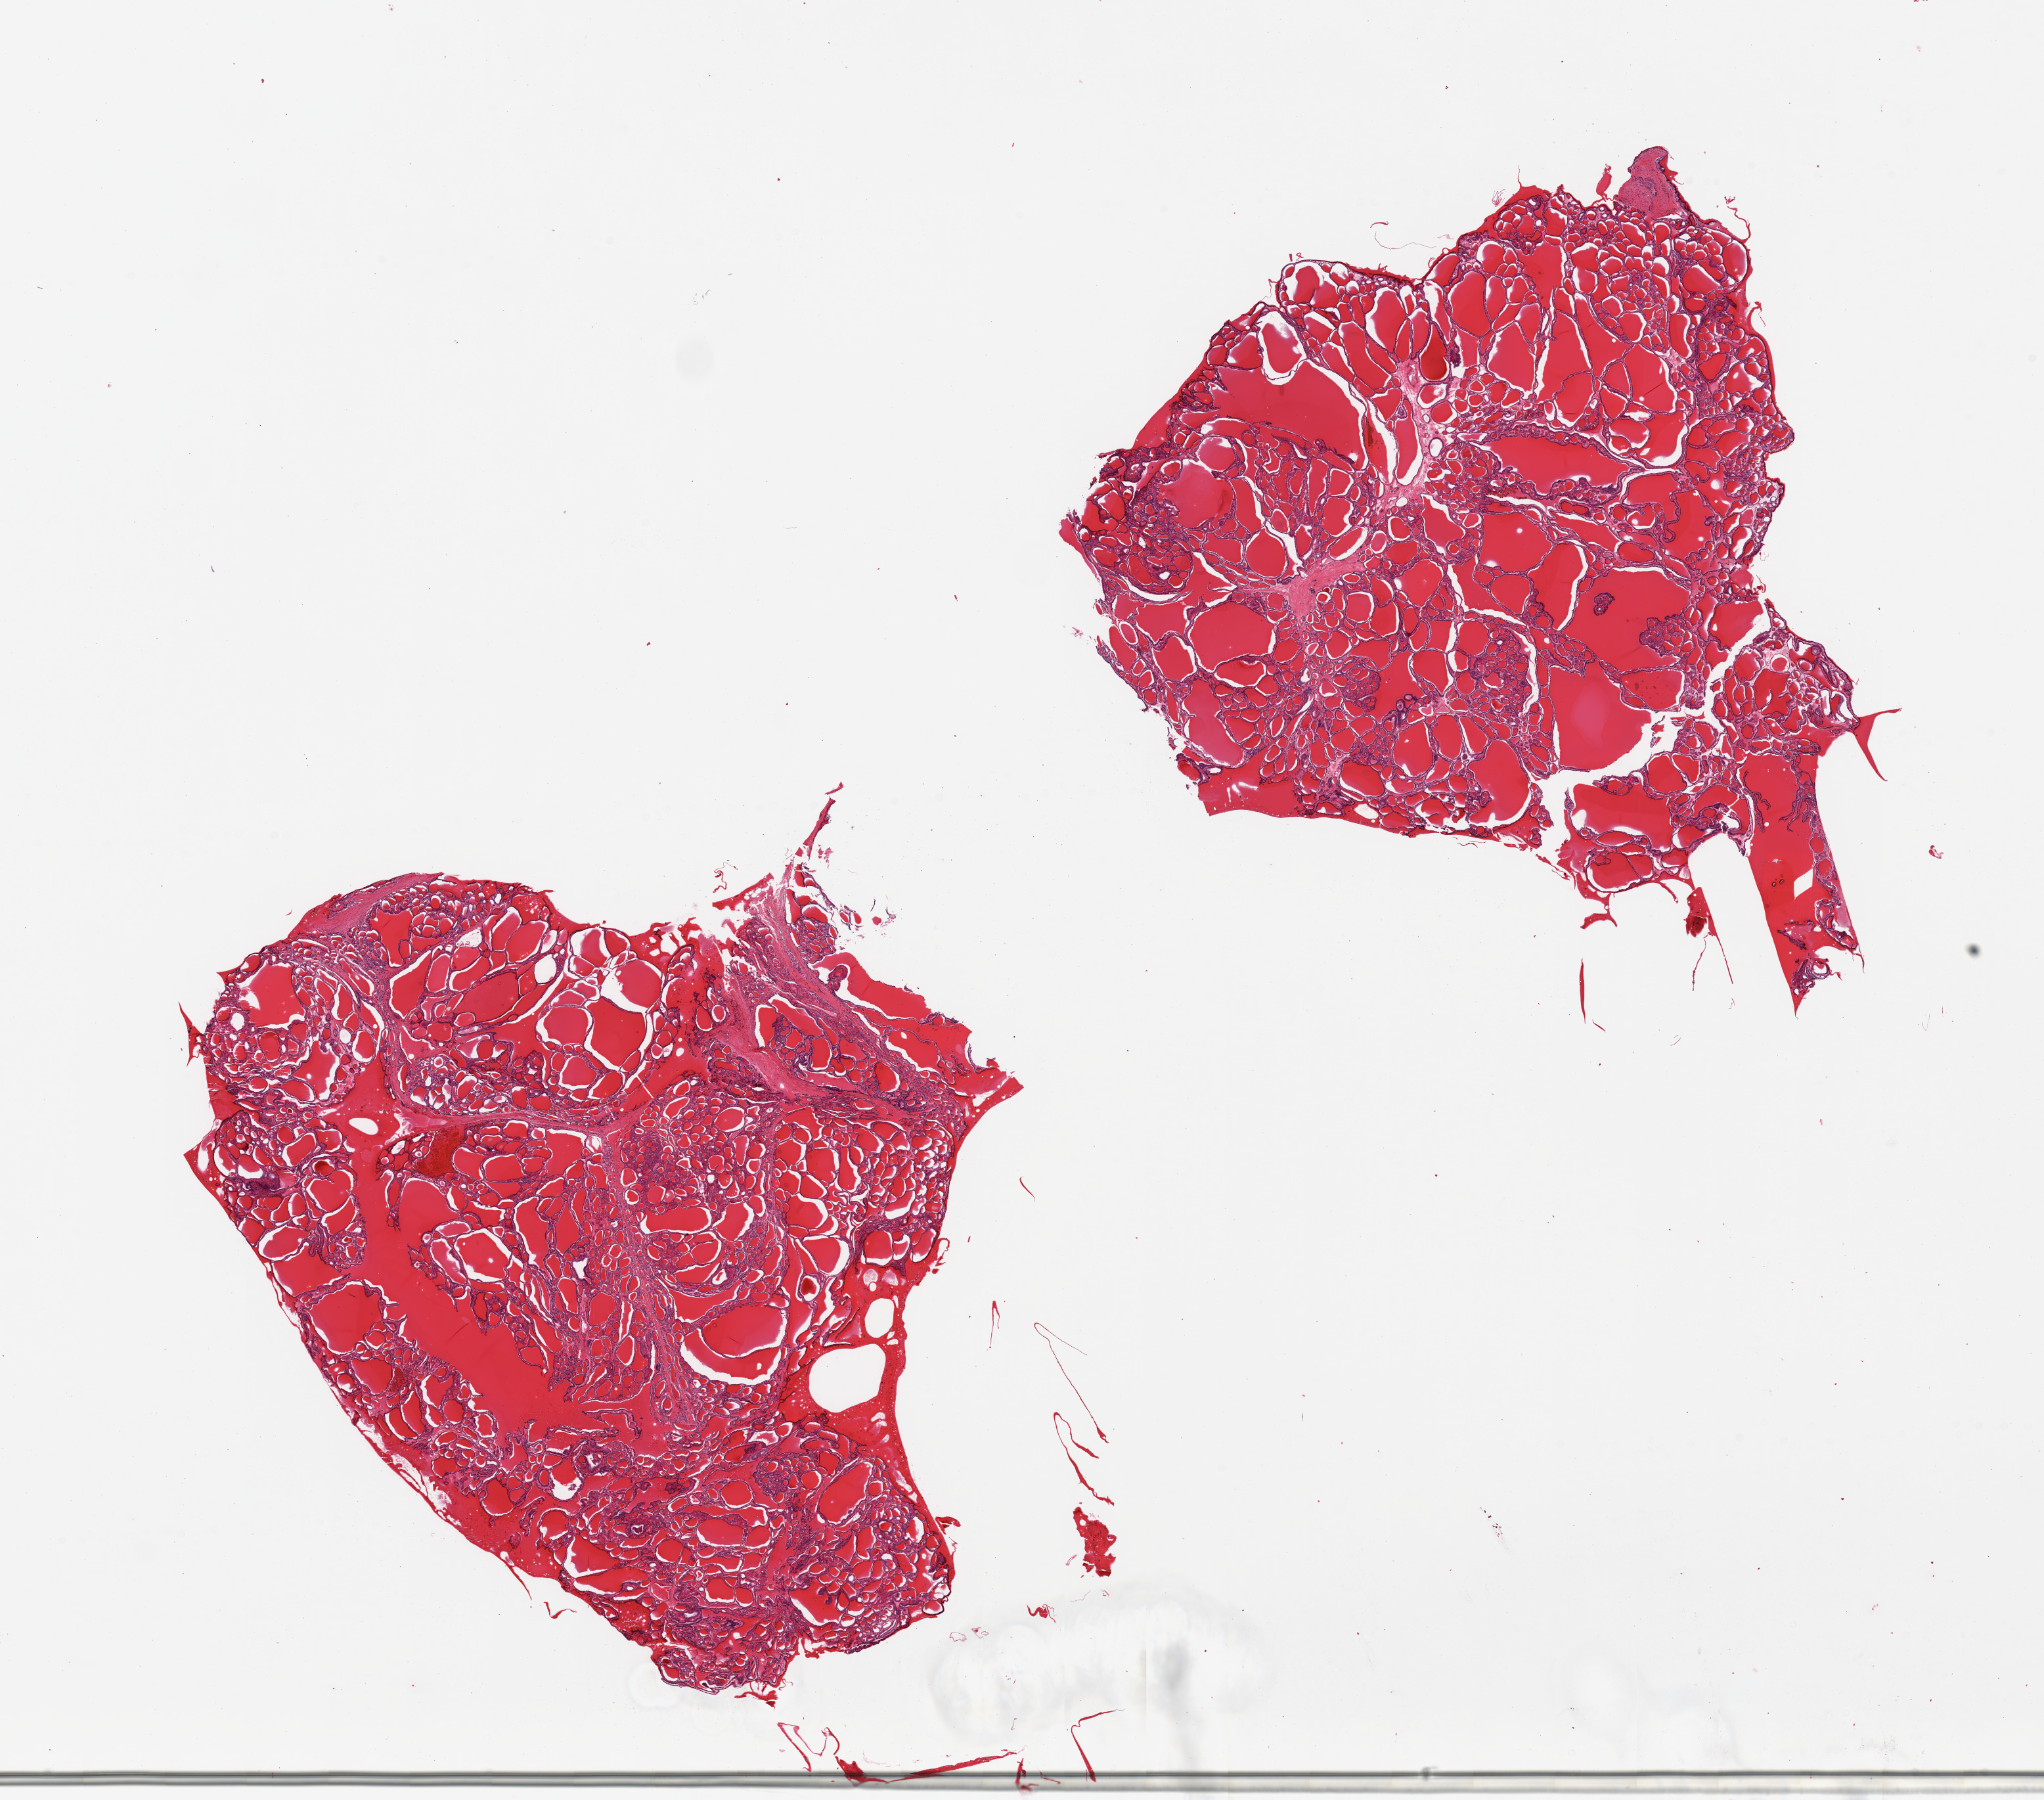
Digitized hematoxylin and eosin (H&E)-stained section — shown as a low-resolution overview of the whole scanned area (about 24.6 x 21.7 mm). PAXgene-fixed, paraffin-embedded tissue. Section of thyroid (target tissue). Donor tissue sample. Donor: male.
- review note (as recorded): 2 pieces